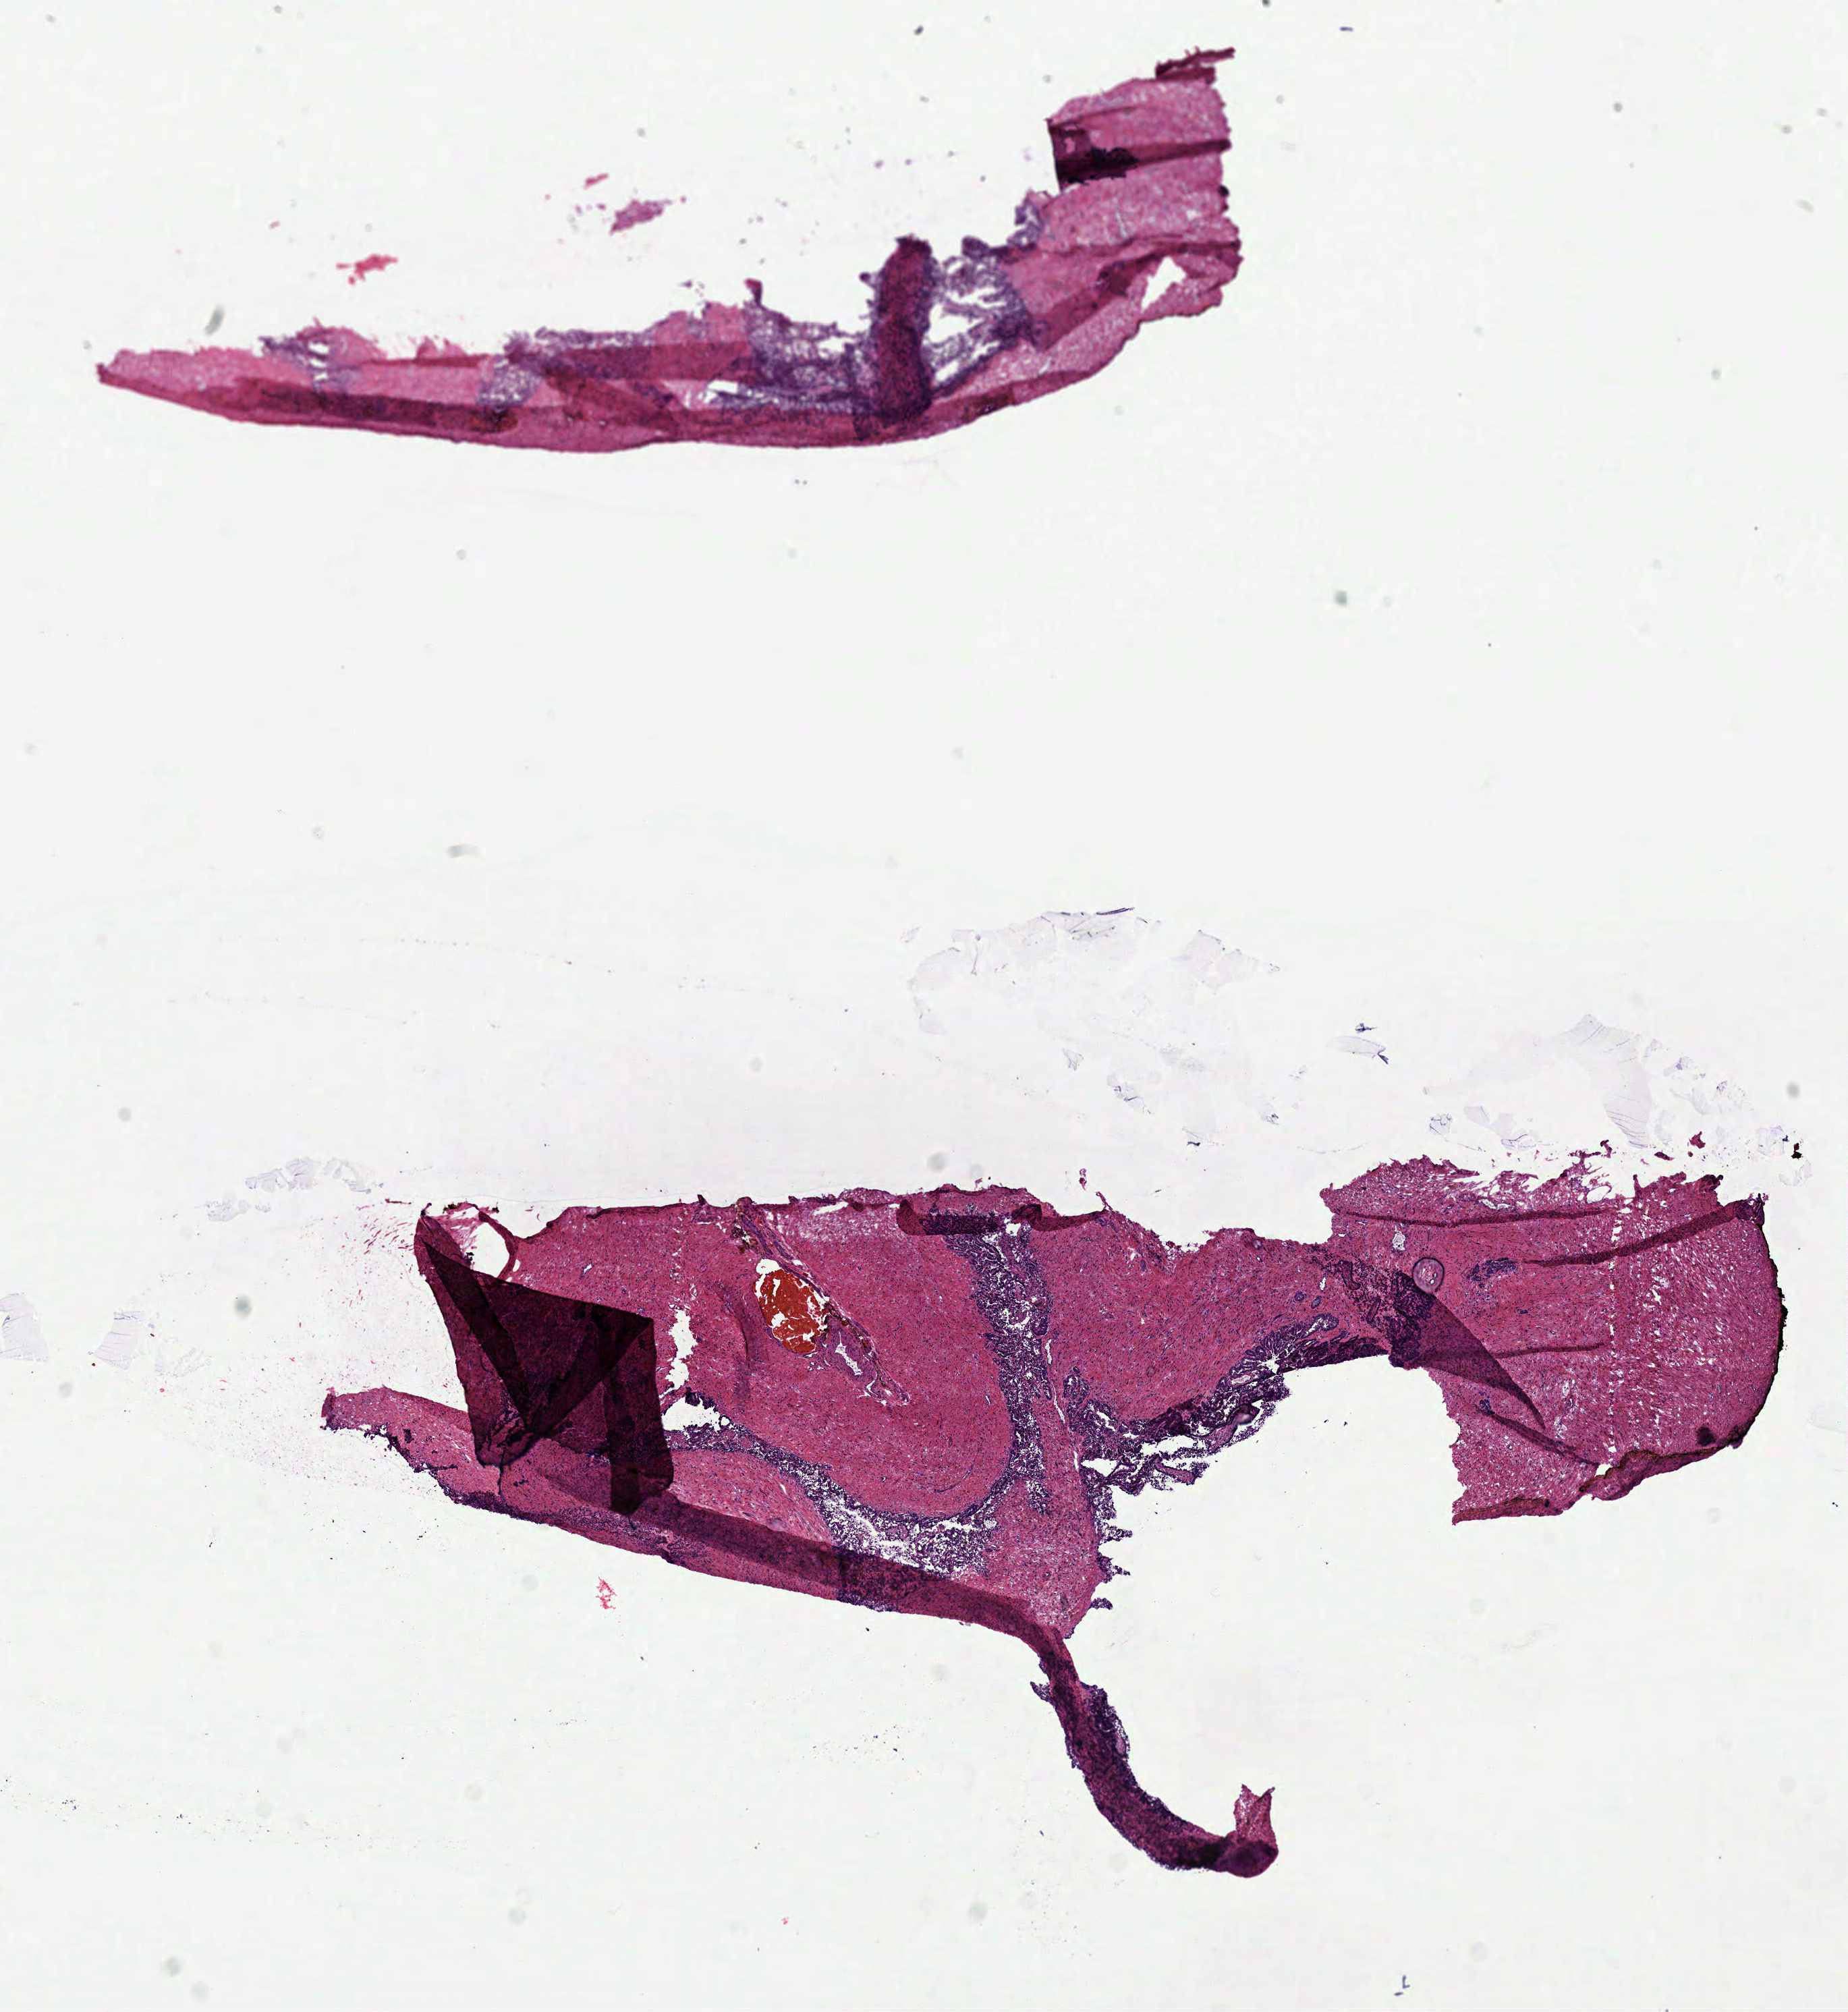
H&E-stained whole-slide image — whole scanned area (about 10.8 x 11.7 mm, slide scanned at 40x) shown as a low-resolution overview. Frozen section from the top of the tissue portion. Prostate, solid tissue normal (non-tumour tissue) sample. Patient: male, age at initial diagnosis 55 years.
This section: solid tissue normal sample (biorepository sample class). Patient diagnosis: Acinar cell carcinoma (prostate gland).